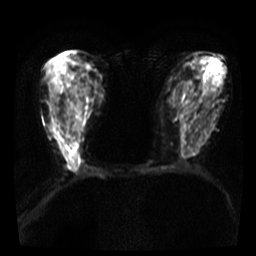
Breast MRI, one axial slice. Position 17 of 36 along the scan axis. Diffusion-weighted series; image 2 of 4 stored at this slice position (different b-values; order by instance number). 3 T. 5 mm slice thickness. 256 × 256 image matrix, field of view 300 × 300 mm. Female patient.
Annotated regions visible in this slice (outlined manually by an expert reader):
- tumour on diffusion-weighted imaging: bounding box <68,141,79,158> (left, top, right, bottom; pixels)